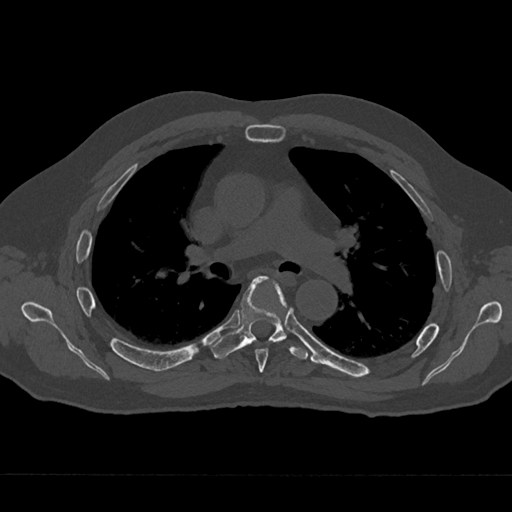
CT including the spine, one axial slice; slice 445 of 797 in the series (ordered by position); reconstruction kernel Br40s/3; 120 kVp; bone window (W 1800 / L 400 HU); 0.5 mm slice thickness; 512 × 512 image matrix. Male patient, age 75 years. Case-level facts recorded for this patient, not image findings: primary cancer: renal; vertebrae with lytic lesions (as recorded): T4.
Structures marked on this image (semi-automatic segmentation, software-assisted and operator-edited):
- T5 vertebra: bounding box (x1, y1, x2, y2) in pixels: (255, 283, 287, 373)
- T6 vertebra: (211, 276, 308, 359)